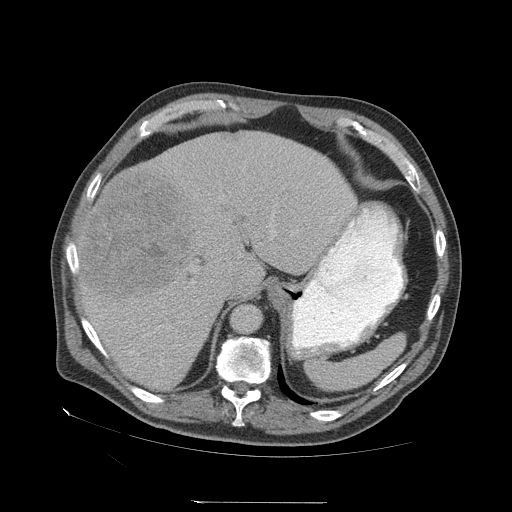
Contrast-enhanced abdominal CT (liver protocol), one axial slice; slice 47 of 83 in the series (ordered by position); 140 kVp; soft-tissue window (W 400 / L 40 HU); 2.5 mm slice thickness; 512 × 512 image matrix, field of view 460 × 460 mm. Case-level facts recorded for this patient, not image findings: diagnosis: hepatocellular carcinoma (patient treated with transarterial chemoembolisation; whether this scan precedes or follows treatment is not stated here); TNM stage (as recorded): Stage-I; Child-Pugh class: A; tumour differentiation: well differentiated; tumour nodularity: uninodular.
Structures marked on this image (semi-automatically segmented with operator editing):
- liver parenchyma outside the tumour (the mass and vessels are separate outlines, so this box may not span the whole liver): bounding box (x1, y1, x2, y2) in pixels: (78, 130, 356, 390)
- mass: (82, 170, 197, 305)
- liver vessels: (84, 203, 354, 356)